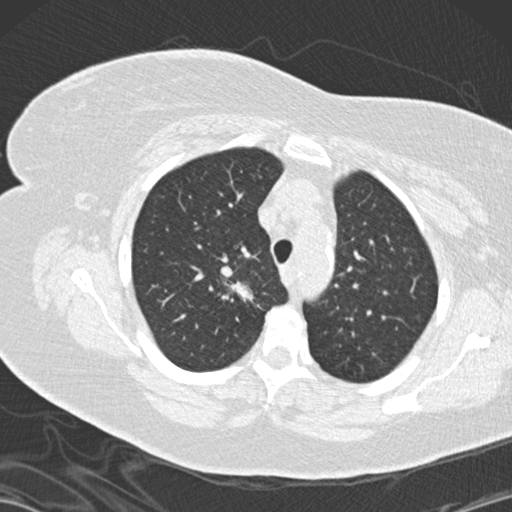
Low-dose screening chest CT, one axial slice. Slice 112 of 146 in the series (ordered by position). Reconstruction kernel B30f. Lung window (W 1500 / L -600 HU). 2 mm slice thickness. 512 × 512 image matrix.
Annotated regions visible in this slice (outlined manually by an expert reader):
- lesion 1 (tumor, upper lobe of right lung): bounding box <221,266,253,301> (left, top, right, bottom; pixels)